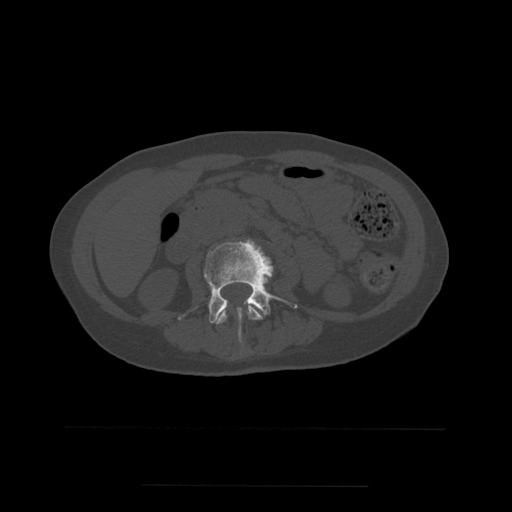
CT including the spine, one axial slice. Position 195 of 544 along the scan axis. Bone window (W 1800 / L 400 HU). 1.25 mm slice thickness. 512 × 512 image matrix, field of view 350 × 350 mm. Patient age 58 years. Case-level facts recorded for this patient, not image findings: primary cancer: lung.
Outlined on this slice (semi-automatic segmentation, software-assisted and operator-edited):
- L2 vertebra: bounding box <216,304,263,325> (left, top, right, bottom; pixels)
- L3 vertebra: <179,239,298,338>